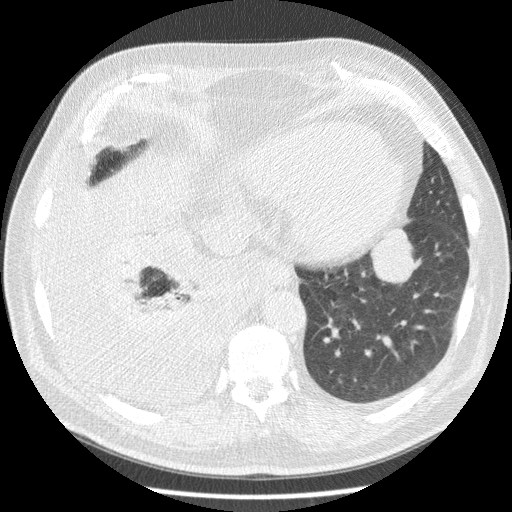
Axial slice from a low-dose chest CT screening exam, third annual screen, lung window (W 1500 / L -600 HU), standard (soft-tissue) reconstruction kernel (STANDARD), 120 kVp, 512 × 512 image matrix. Male participant, aged 63 years at enrolment. Current smoker at enrolment.
• Lesion marked by an expert reader, bounding box [x1, y1, x2, y2] px = [353, 222, 419, 291].
• The exam's reader record, not a measurement of the box and not confirmed to be the same lesion: non-calcified nodule or mass ≥4 mm, left lower lobe, 34 × 31 mm, smooth margins, soft tissue attenuation, pre-existing on the prior screen: yes; interval growth: yes.
• Official screen result: positive, other.